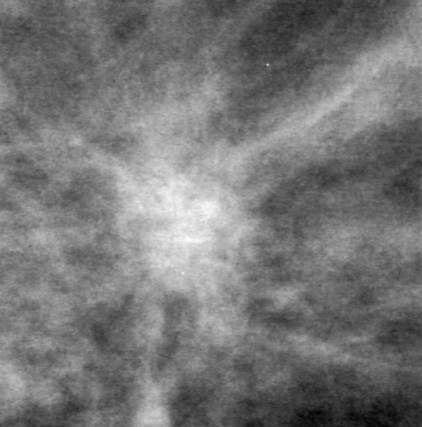
Region of interest cut from a scanned film mammogram (one marked finding); left breast; MLO view; BI-RADS breast density category 3 (scale 1–4).
Marked abnormality: mass, shape architectural distortion, margins ill defined; BI-RADS assessment category 4; pathology result (as recorded, not read from the image): benign.